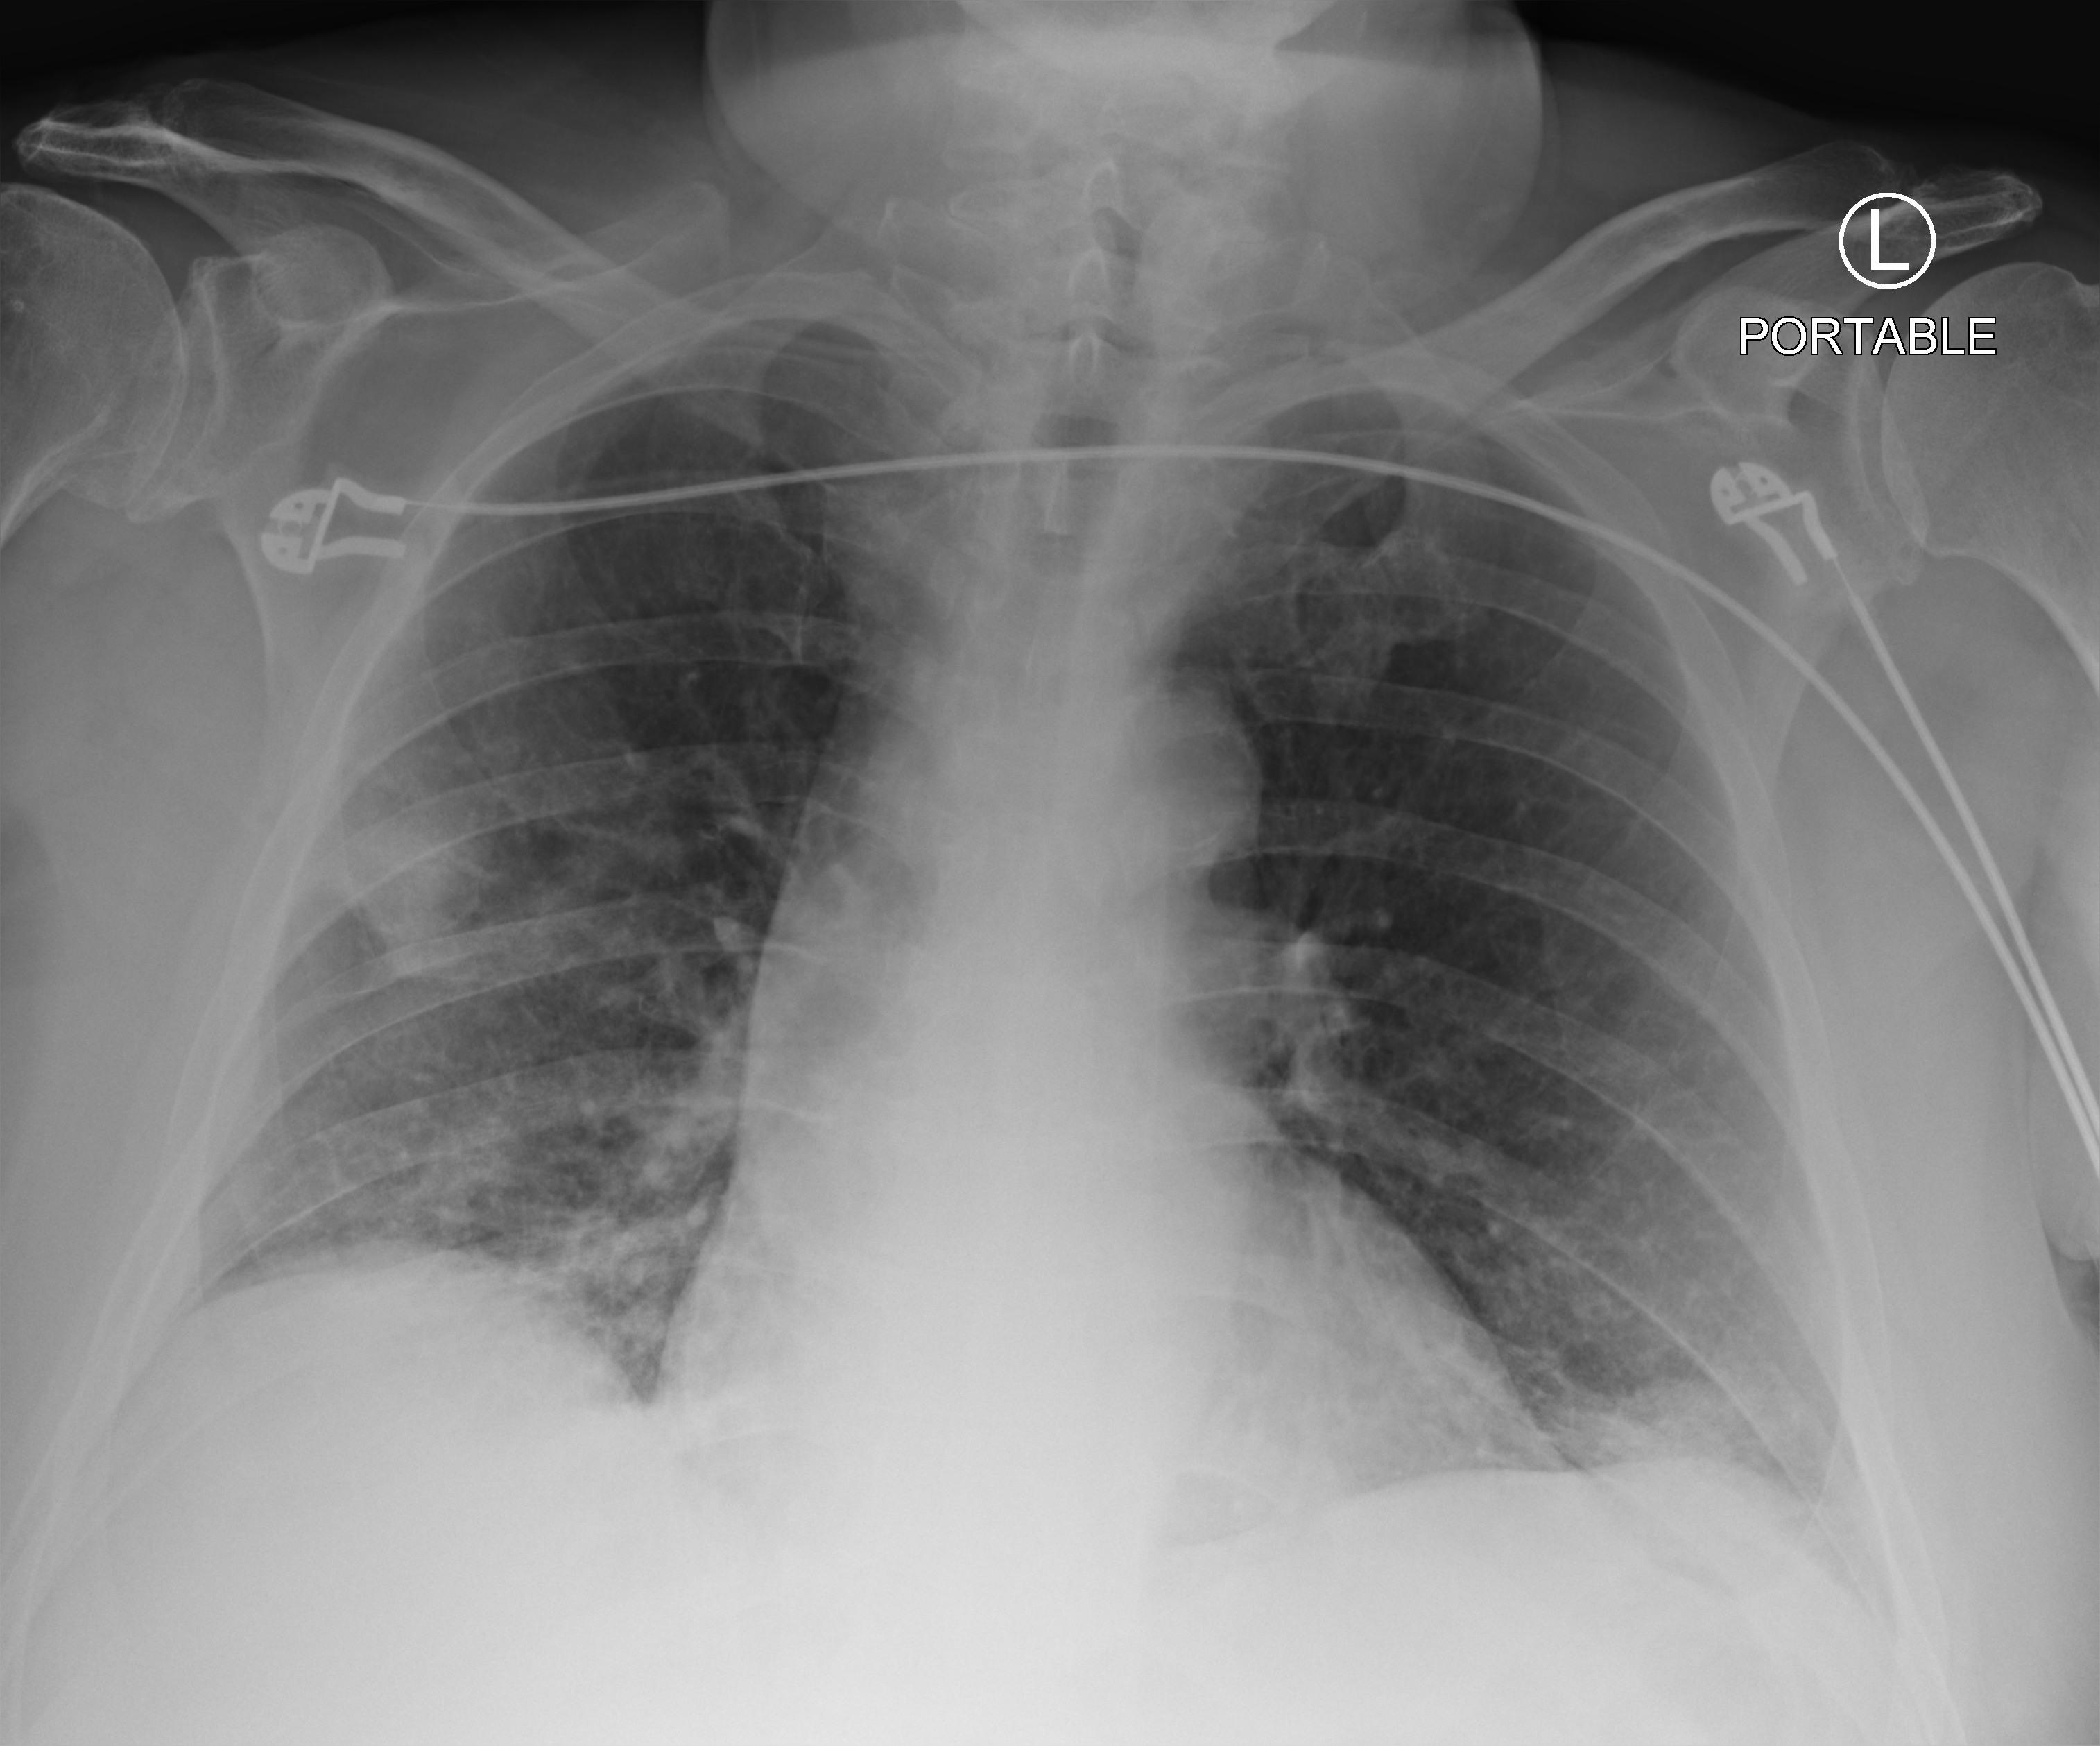
Chest X-ray (portable); anteroposterior (AP) projection. Patient hospitalised with COVID-19; male, aged 60–74 years.
Hospital-stay facts (about this admission, not read from this image; timing relative to this image not recorded): mechanically ventilated during this hospital stay: no.